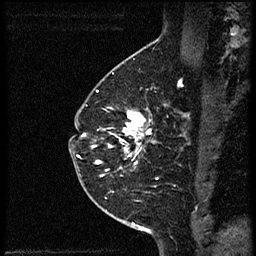
Breast MRI (dynamic contrast-enhanced), one sagittal slice. Position 40 of 56 along the scan axis. Dynamic contrast-enhanced study with each time point stored as its own series, time point 2 of 4 at this slice position (early post-contrast, ordered by acquisition time). 1.5 T. TE 4.2 ms, TR 18.9 ms. 2 mm slice thickness. 256 × 256 image matrix. Female patient. Case-level facts recorded for this patient, not image findings: setting: breast cancer imaged before/during neoadjuvant chemotherapy; receptor status: HER2-positive.
Structures marked on this image (semi-automatic segmentation, software-assisted and operator-edited):
- analysis volume of interest (the breast-tissue region the enhancement analysis was run in; not a lesion): box from (x=78, y=87) to (x=161, y=189) px
- tumour enhancement mask (voxels above the 100 % enhancement threshold inside the analysis volume of interest): (x=84, y=109)–(x=152, y=171)